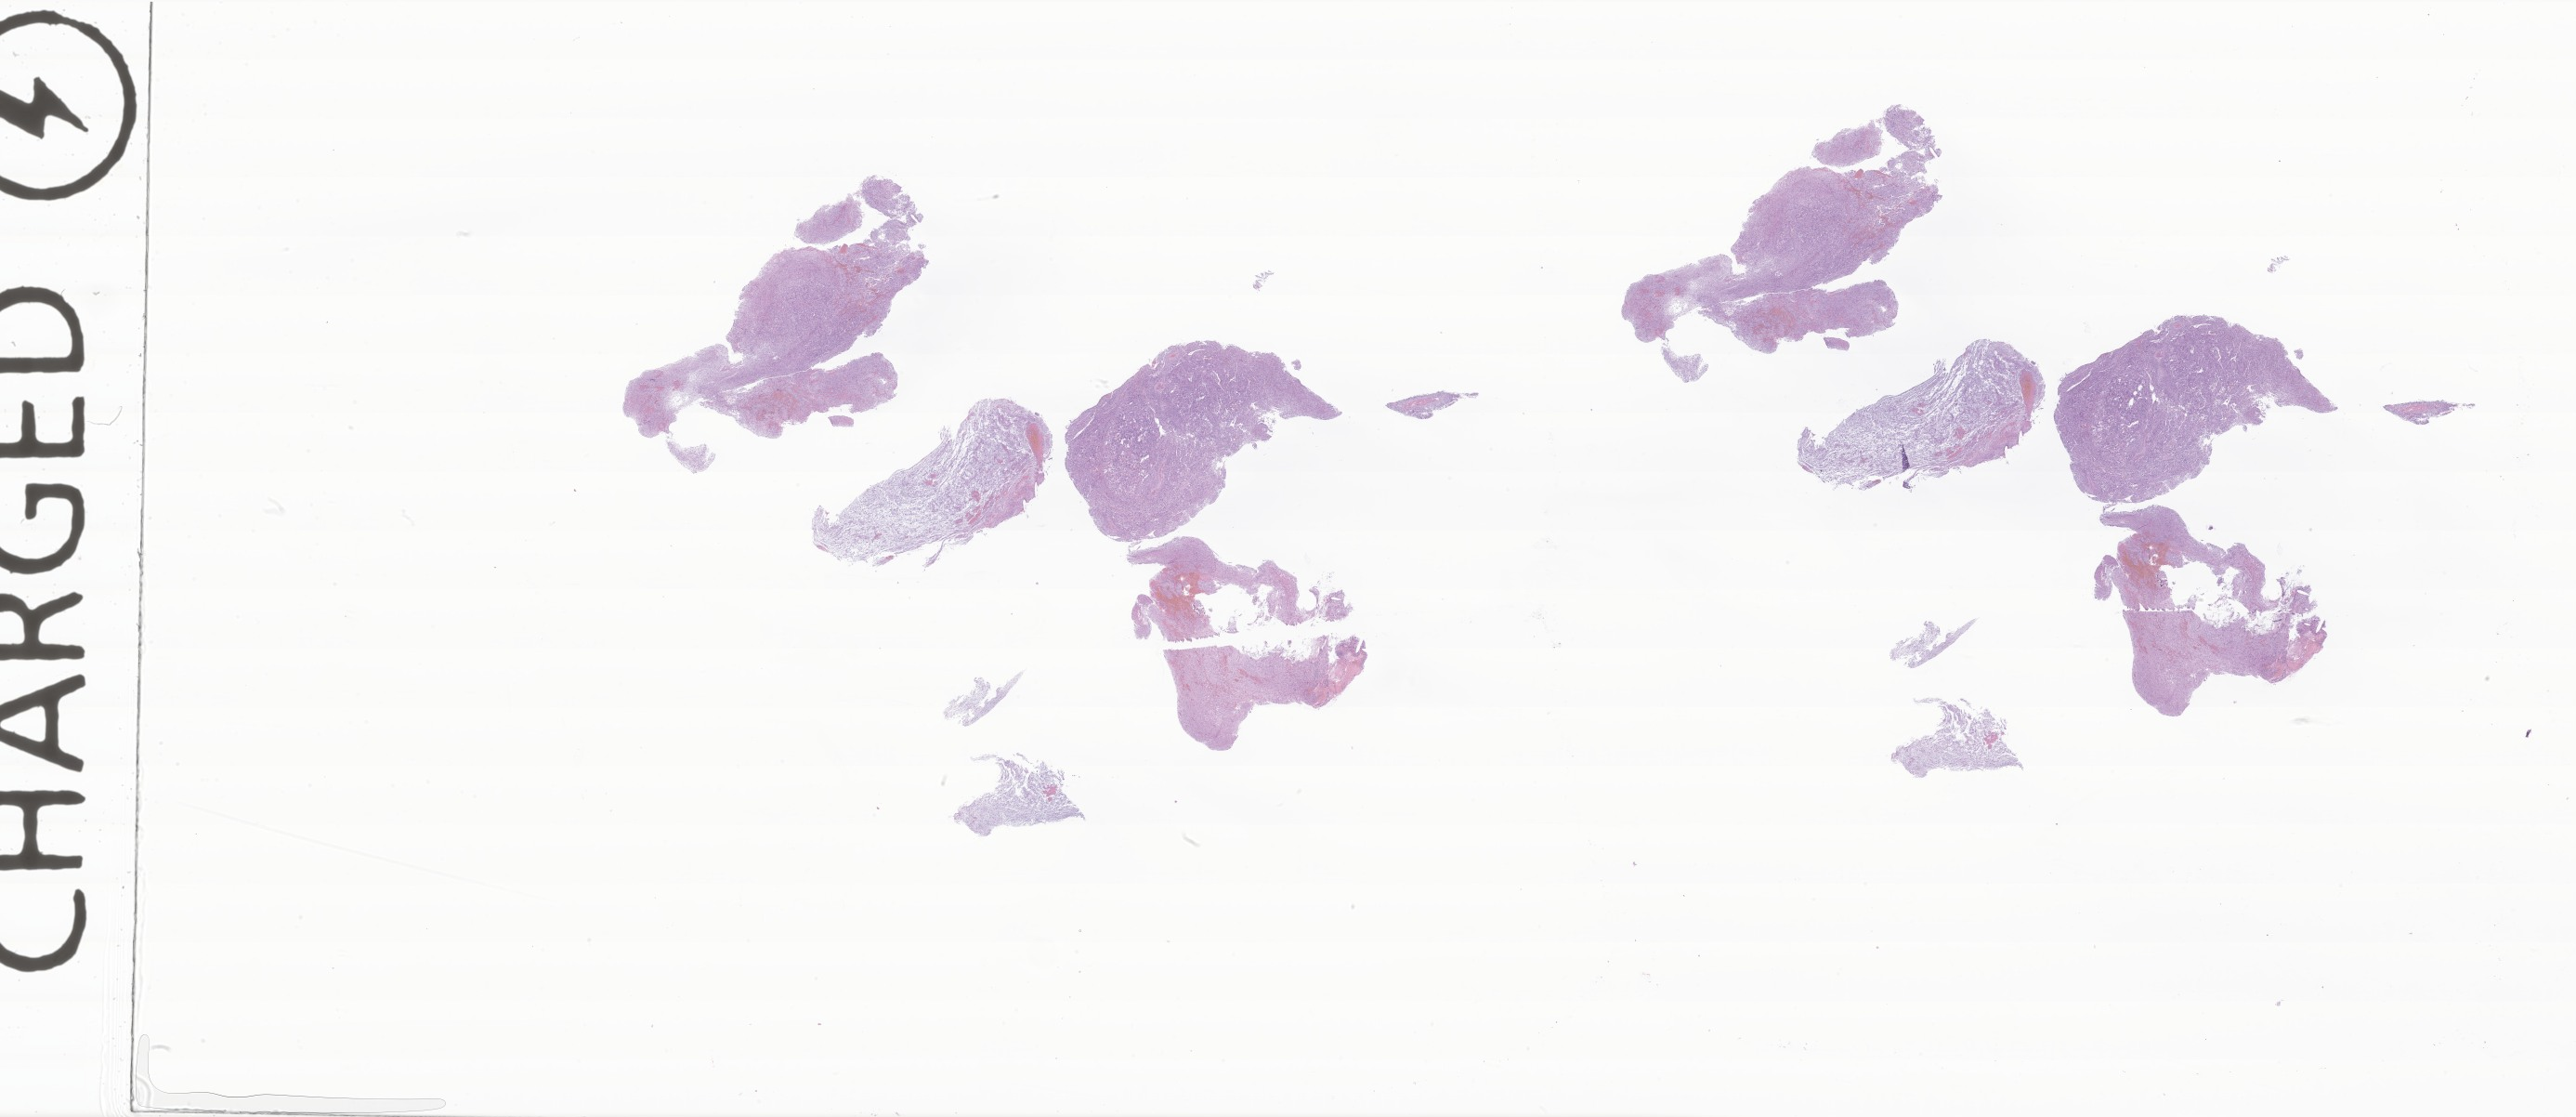
Whole-slide image, haematoxylin and eosin stain of tumor tissue from the frontal lobe — whole scanned area (about 46.8 x 20.3 mm) shown as a low-resolution overview. FFPE section. Patient male; age 139 months.
* diagnosis (ICD-O-3 morphology term): Glioma, malignant